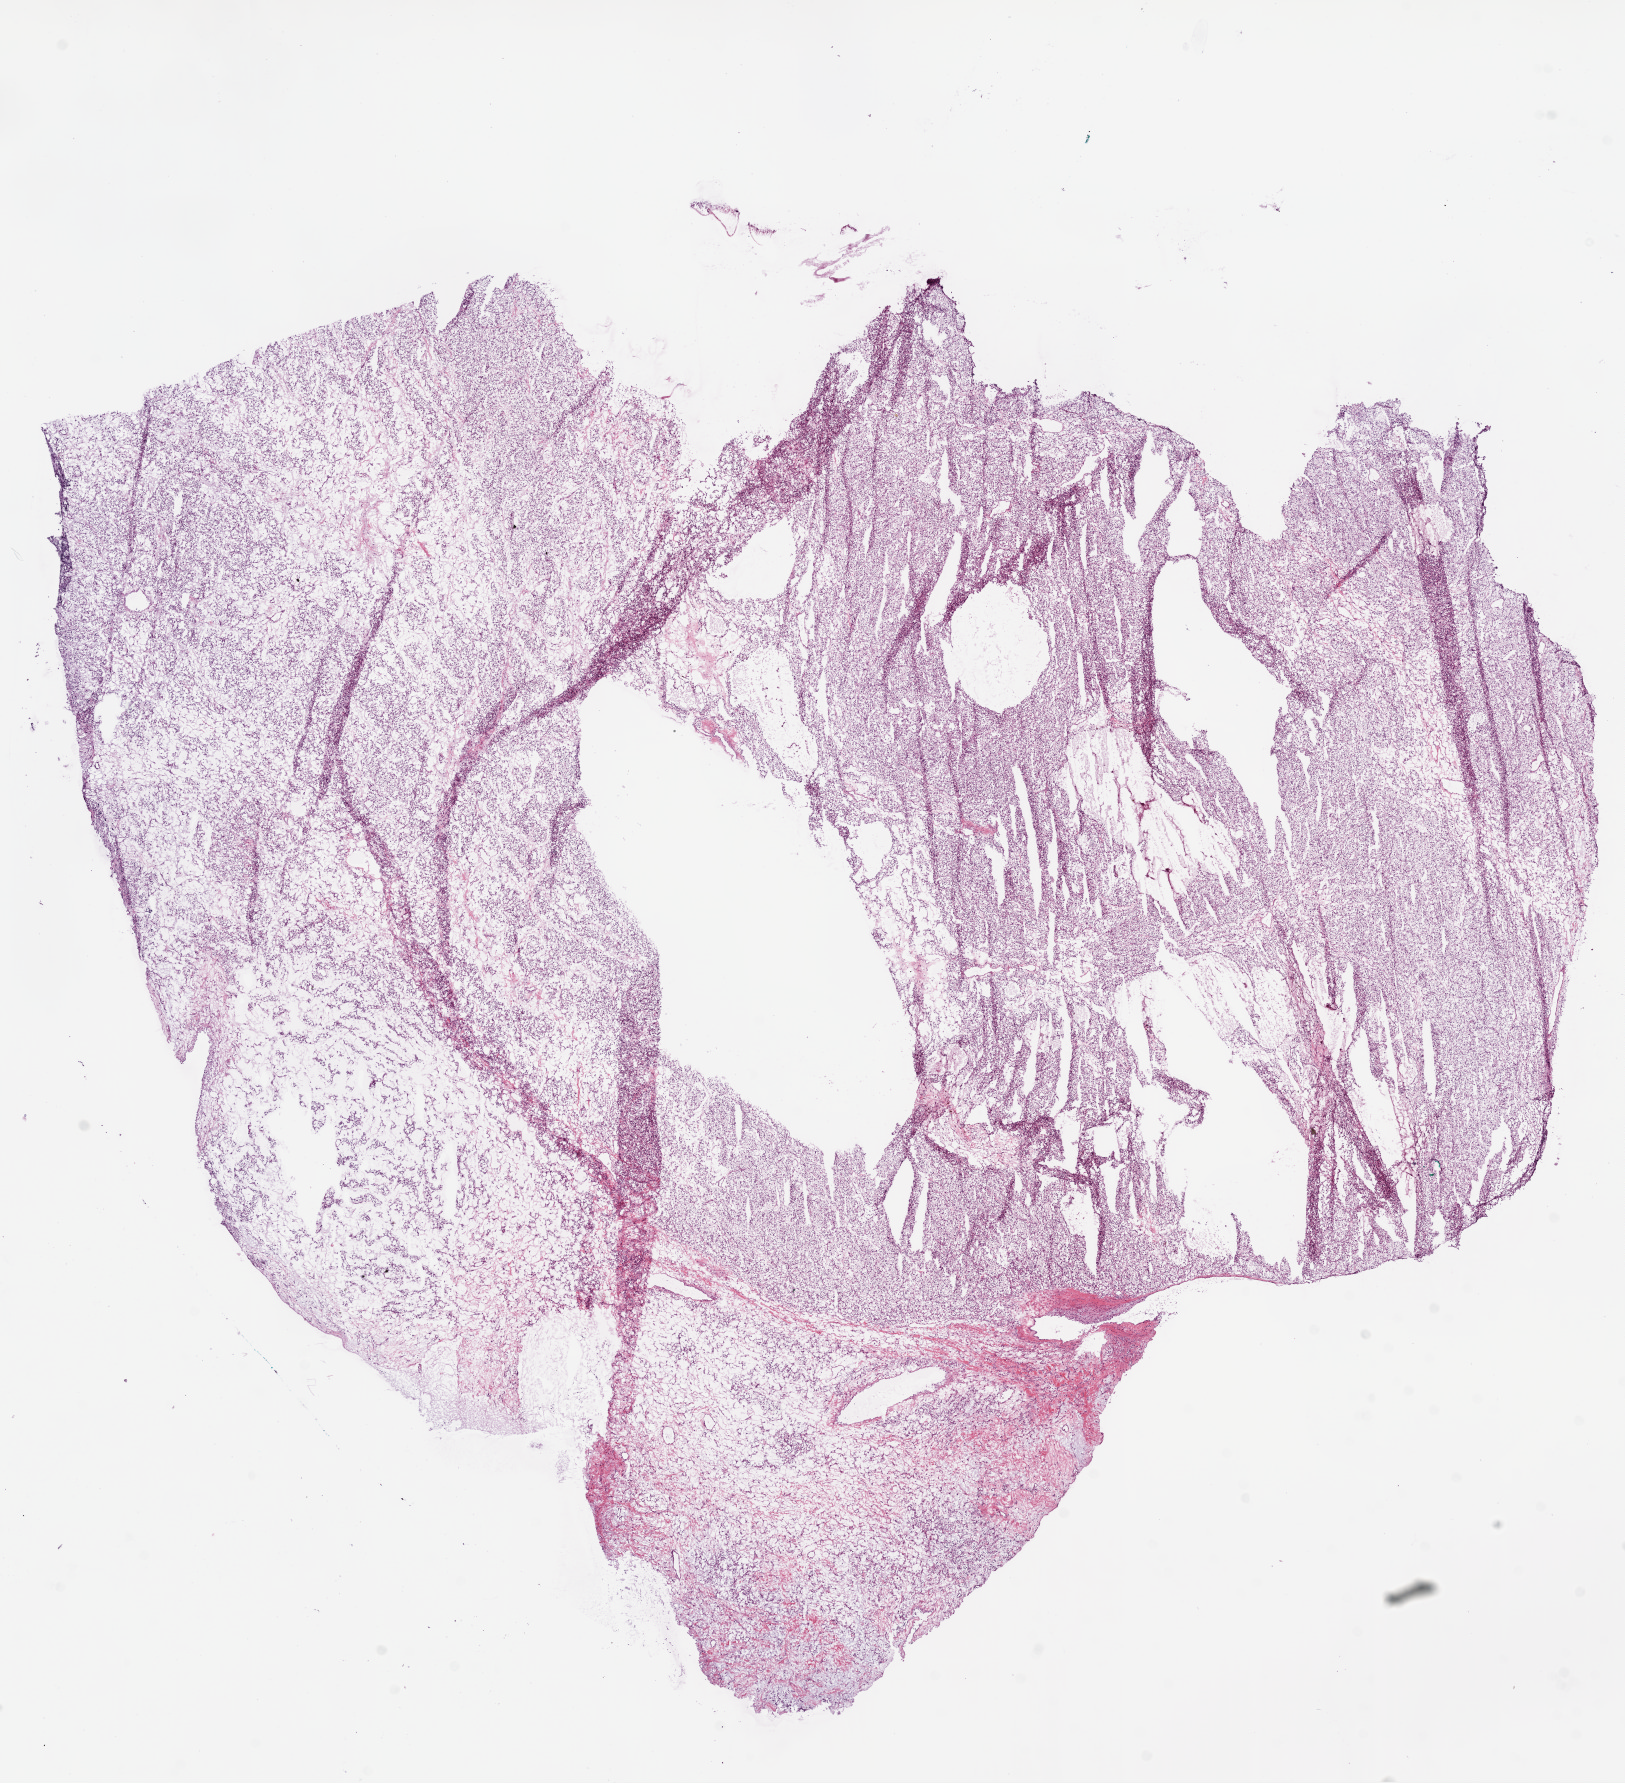
Hematoxylin and eosin (H&E) stained whole-slide image, low-resolution overview of the scanned area, about 13.0 x 14.3 mm (from a 20x scan). Frozen section from the bottom of the tissue portion. Primary tumour sample from the kidney. Patient: female, age at initial diagnosis 41 years. Histologic grade: G2 (moderately differentiated). Slide review estimates, as recorded: tumour cells 80%, tumour nuclei 80%, normal cells 0%, stromal cells 20%, necrosis 0%.
AJCC pathologic stage: I. Pathologic diagnosis: Clear cell adenocarcinoma, NOS.